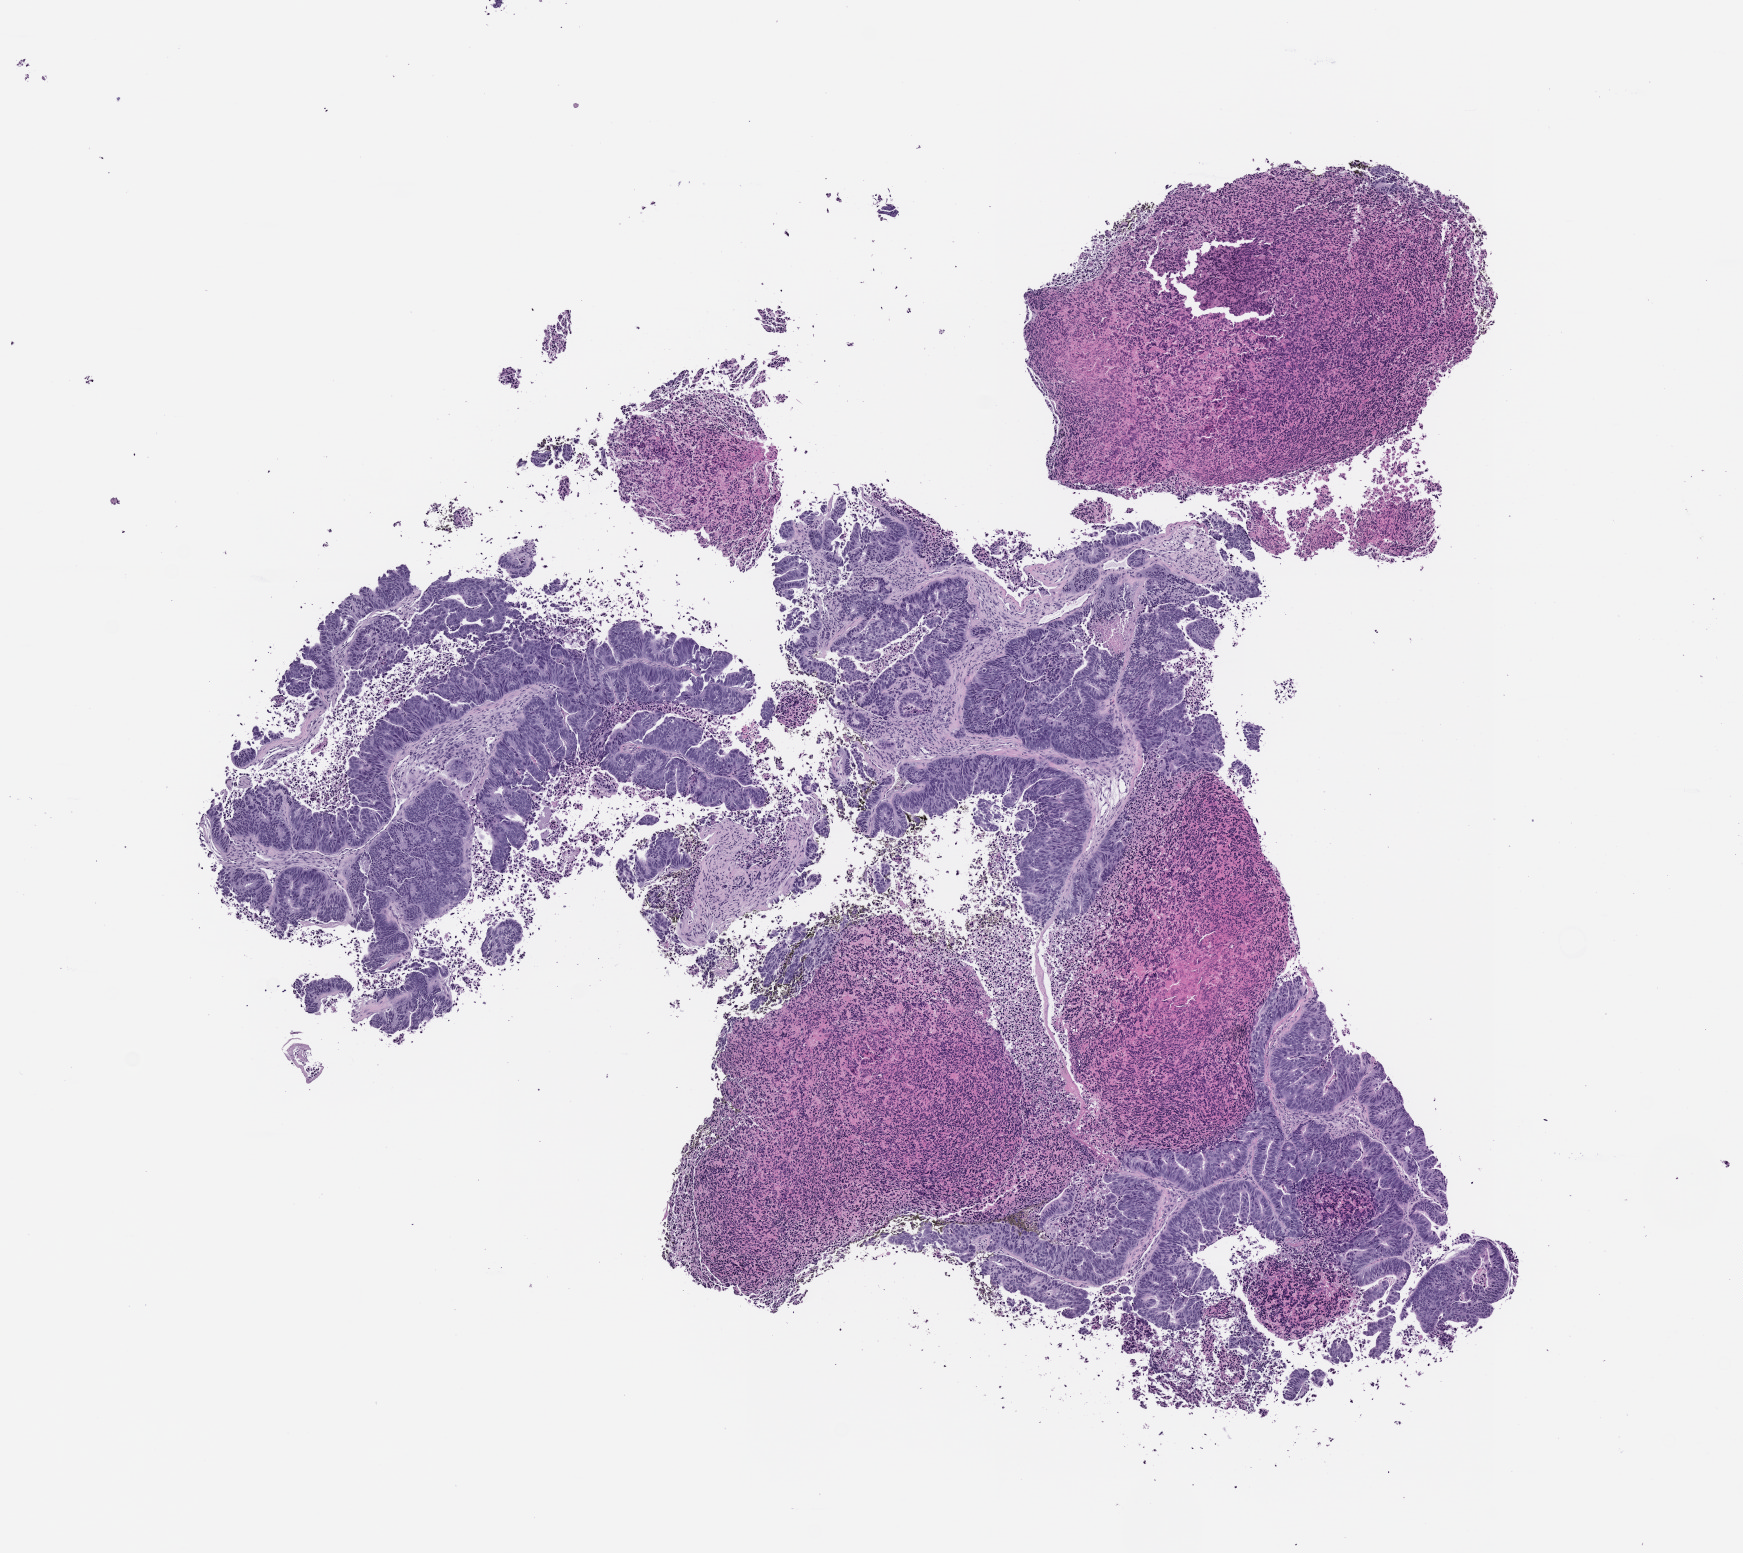
Hematoxylin and eosin (H&E) whole-slide image of a patient-derived xenograft (PDX) tumor grown in a mouse, passage 1 — low-resolution overview of the scanned area, about 7.0 x 6.2 mm, formalin-fixed paraffin-embedded section, tumor site category: colon.
Originating patient diagnosis: Colon Adenocarcinoma.